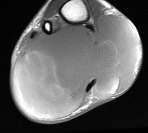
MRI of an extremity soft-tissue mass, one axial slice. Position 25 of 76 along the scan axis. MR volume resampled by the dataset authors to the PET/CT grid (not the native acquisition matrix). 148 × 133 image matrix, field of view 145 × 130 mm. Male patient. Case-level facts recorded for this patient, not image findings: histological type: liposarcoma - round cell; grade: high; site of the primary tumour: right calf.
Outlined on this slice (expert contour drawn on MRI and transferred to this co-registered scan by the dataset authors):
- gross tumour volume (mass): bounding box [x1, y1, x2, y2] px = [13, 14, 141, 116]